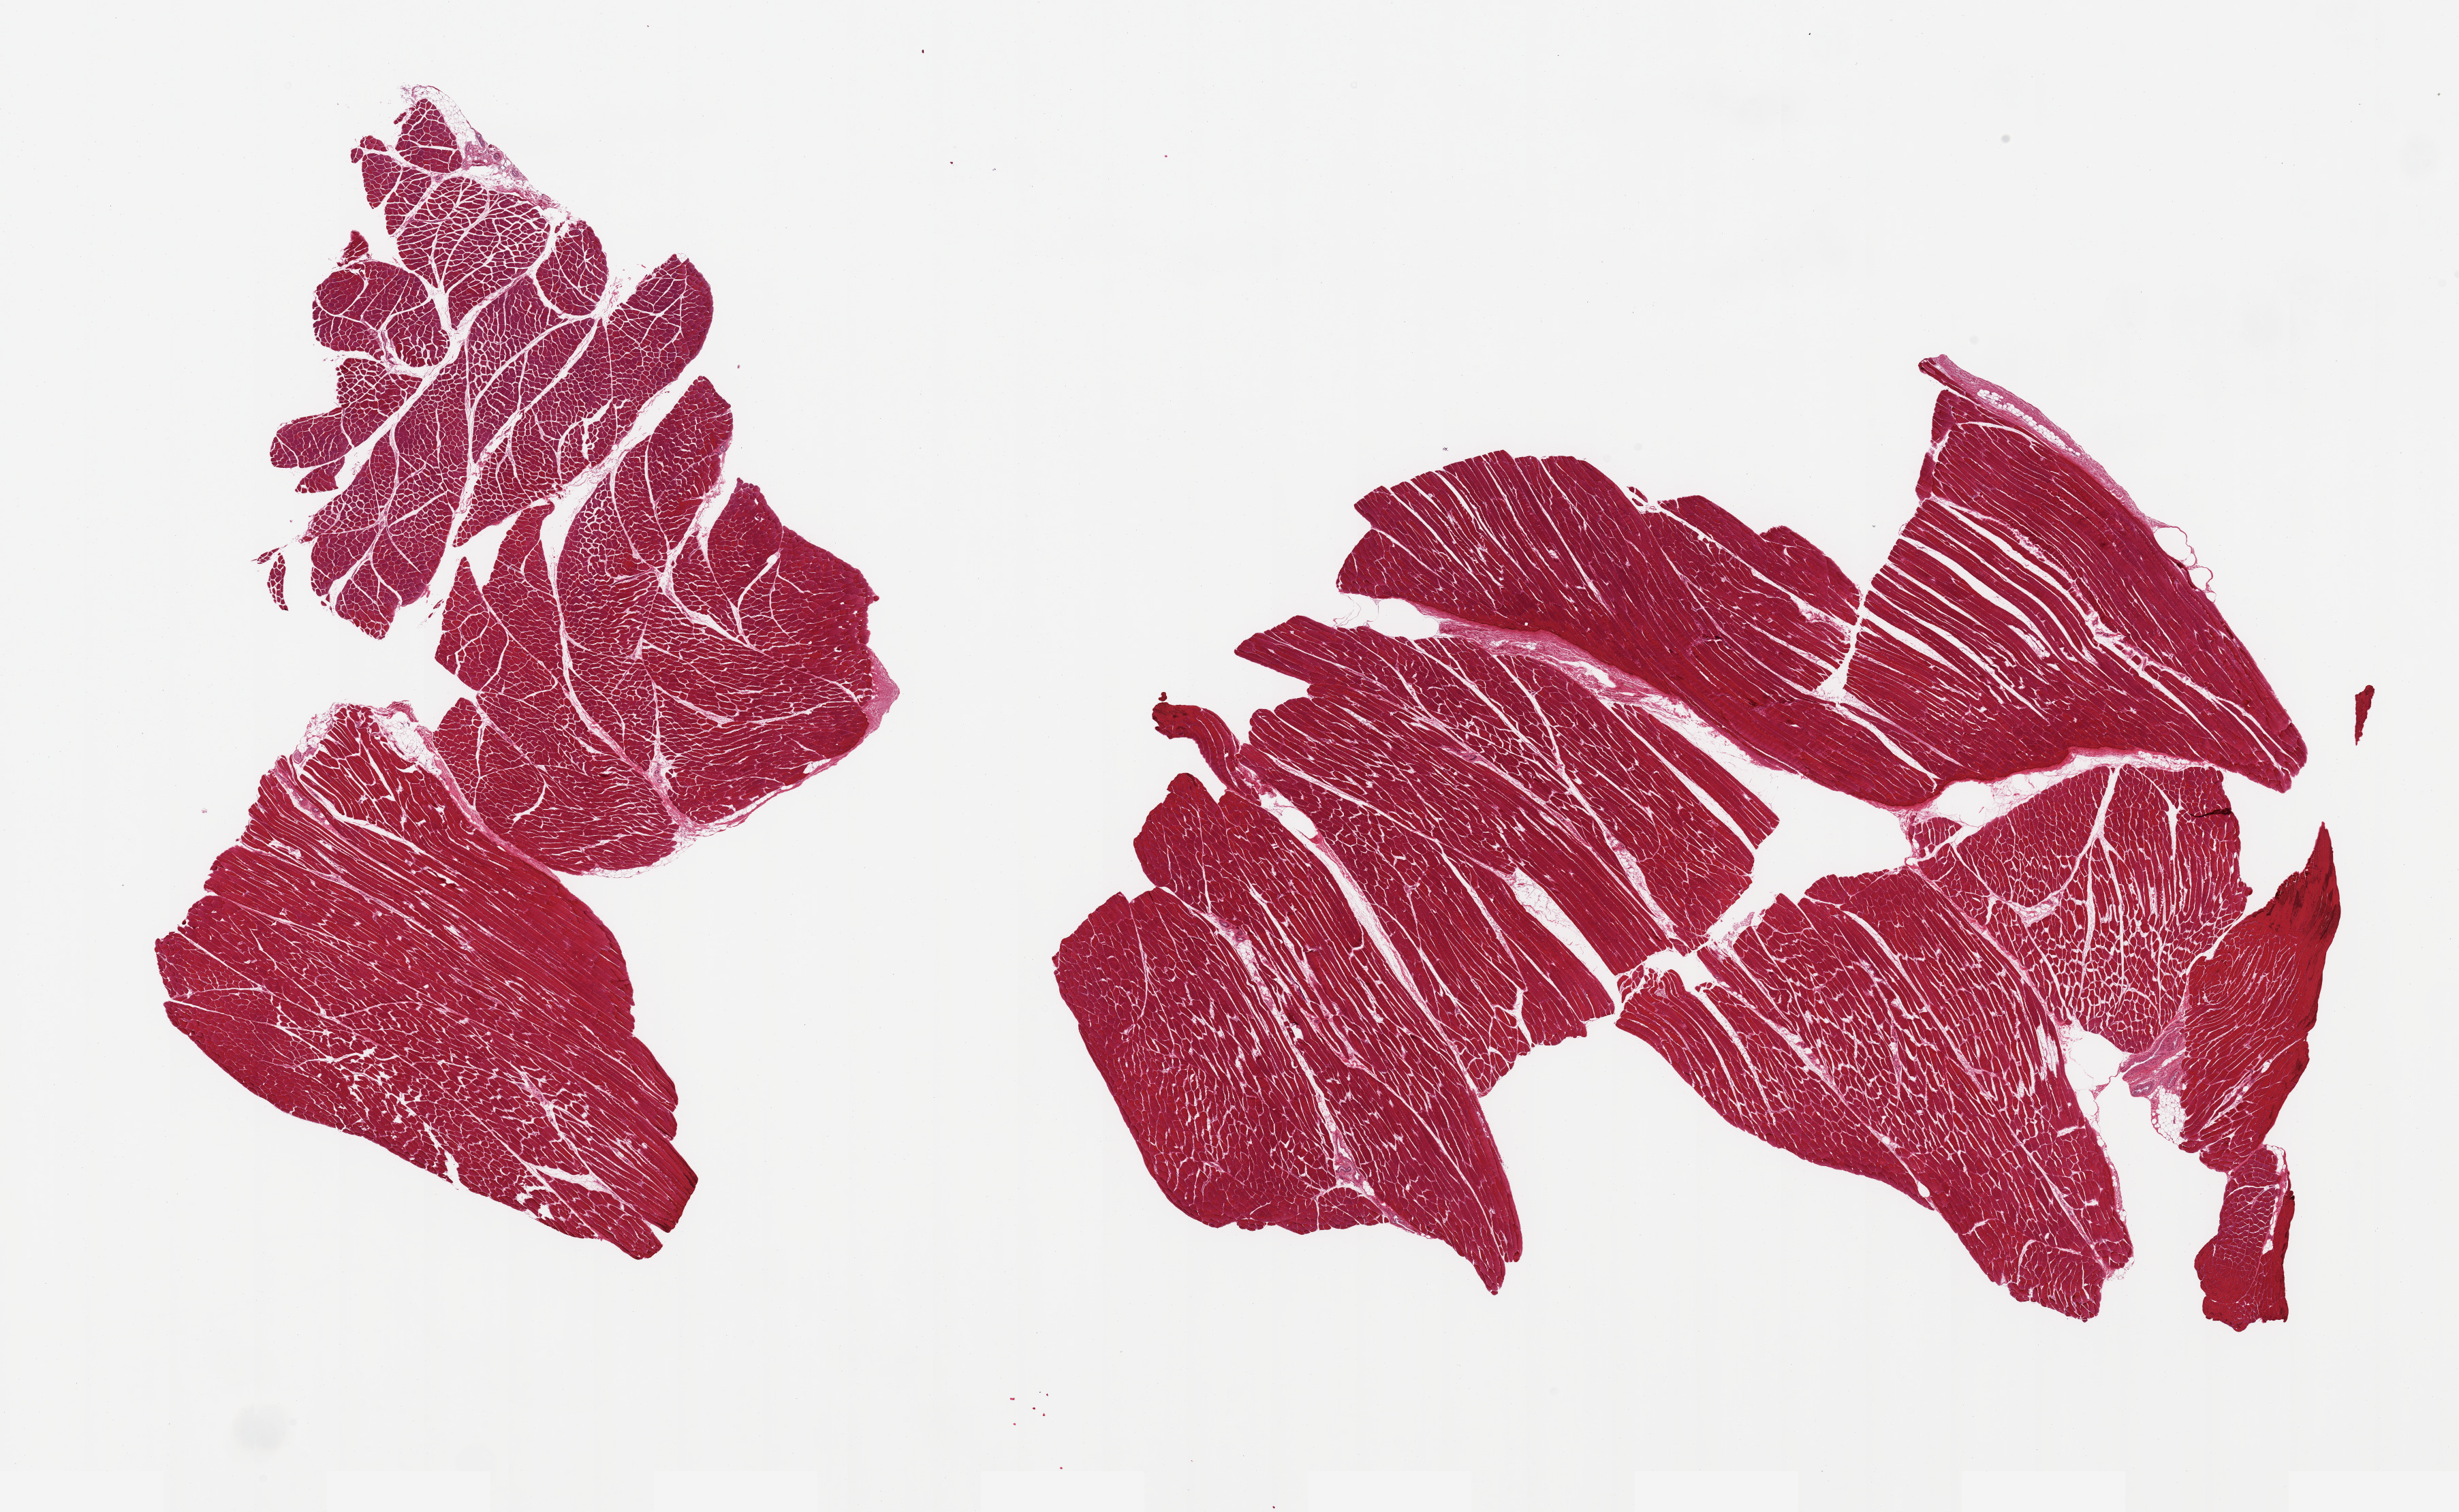
Haematoxylin and eosin whole-slide image, brightfield, whole scanned area (about 28.5 x 17.6 mm) shown as a low-resolution overview. PAXgene-fixed paraffin-embedded (PFPE) section. Sampled site (target tissue): skeletal muscle. Donor tissue sample. Male donor.
• pathologist's review note for this sample: 2 pieces